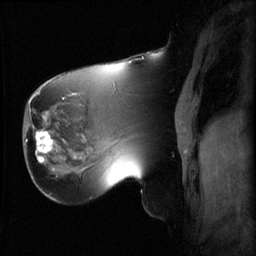
Breast MRI (dynamic contrast-enhanced), one sagittal slice; position 21 of 60 along the scan axis; 3 images stored at this slice position (order not interpretable as contrast timing); 1.5 T; TE 4.2 ms, TR 8.2 ms; 2.2 mm slice thickness; 256 × 256 image matrix. Patient: female, 62 years.
Annotated regions visible in this slice (semi-automatic segmentation, software-assisted and operator-edited):
- analysis volume of interest (the breast-tissue region the enhancement analysis was run in; not a lesion): bounding box [x1, y1, x2, y2] px = [26, 126, 59, 165]
- tumour enhancement mask (voxels above the 70 % enhancement threshold inside the analysis volume of interest): [26, 130, 53, 163]